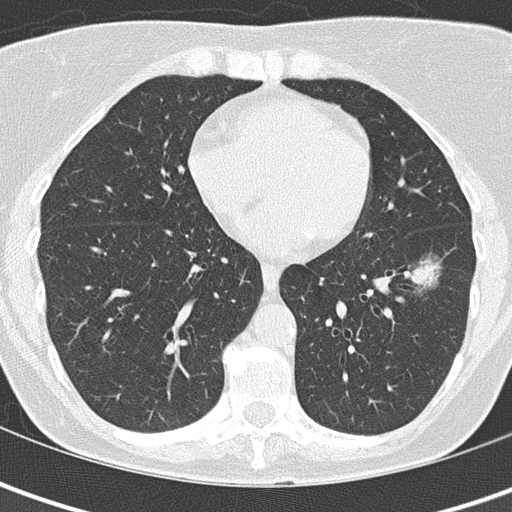
Low-dose screening chest CT, axial slice, first (baseline) screen, lung window (W 1500 / L -600 HU), 2 mm slice thickness, slice 91 of 149 in the series, 512 × 512 image matrix. Female, age 61 years at enrolment.
- Lesion marked by an expert reader, bounding box <380,248,454,305> (left, top, right, bottom; pixels).
- The exam's reader record, not a measurement of the box and not confirmed to be the same lesion: non-calcified nodule or mass ≥4 mm, left lower lobe, 29 × 16 mm, ground glass attenuation.
- Lung cancer was diagnosed 259 days after this screen: bronchiolo-alveolar adenocarcinoma, NOS, left lower lobe, well differentiated (G1), stage IA (AJCC 6th edition), 10 mm at pathology.